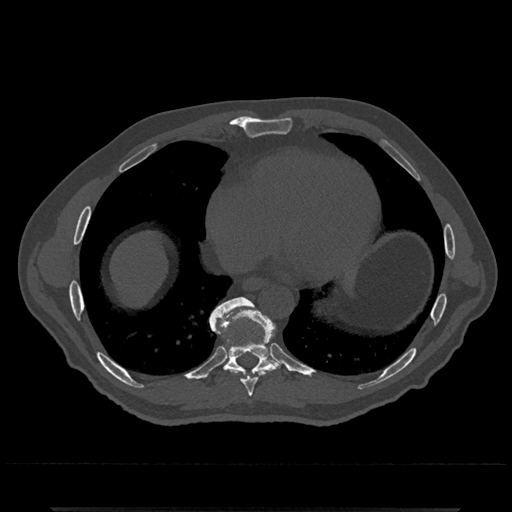
CT including the spine, one axial slice. Position 639 of 797 along the scan axis. 120 kVp. Bone window (W 1800 / L 400 HU). 512 × 512 image matrix, field of view 393 × 393 mm. Male patient, age 67 years. From the clinical record (not read from this slice): primary cancer: prostate.
Outlined on this slice (semi-automatically segmented with operator editing):
- T8 vertebra: bounding box <214,331,263,397> (left, top, right, bottom; pixels)
- T9 vertebra: <210,297,280,375>